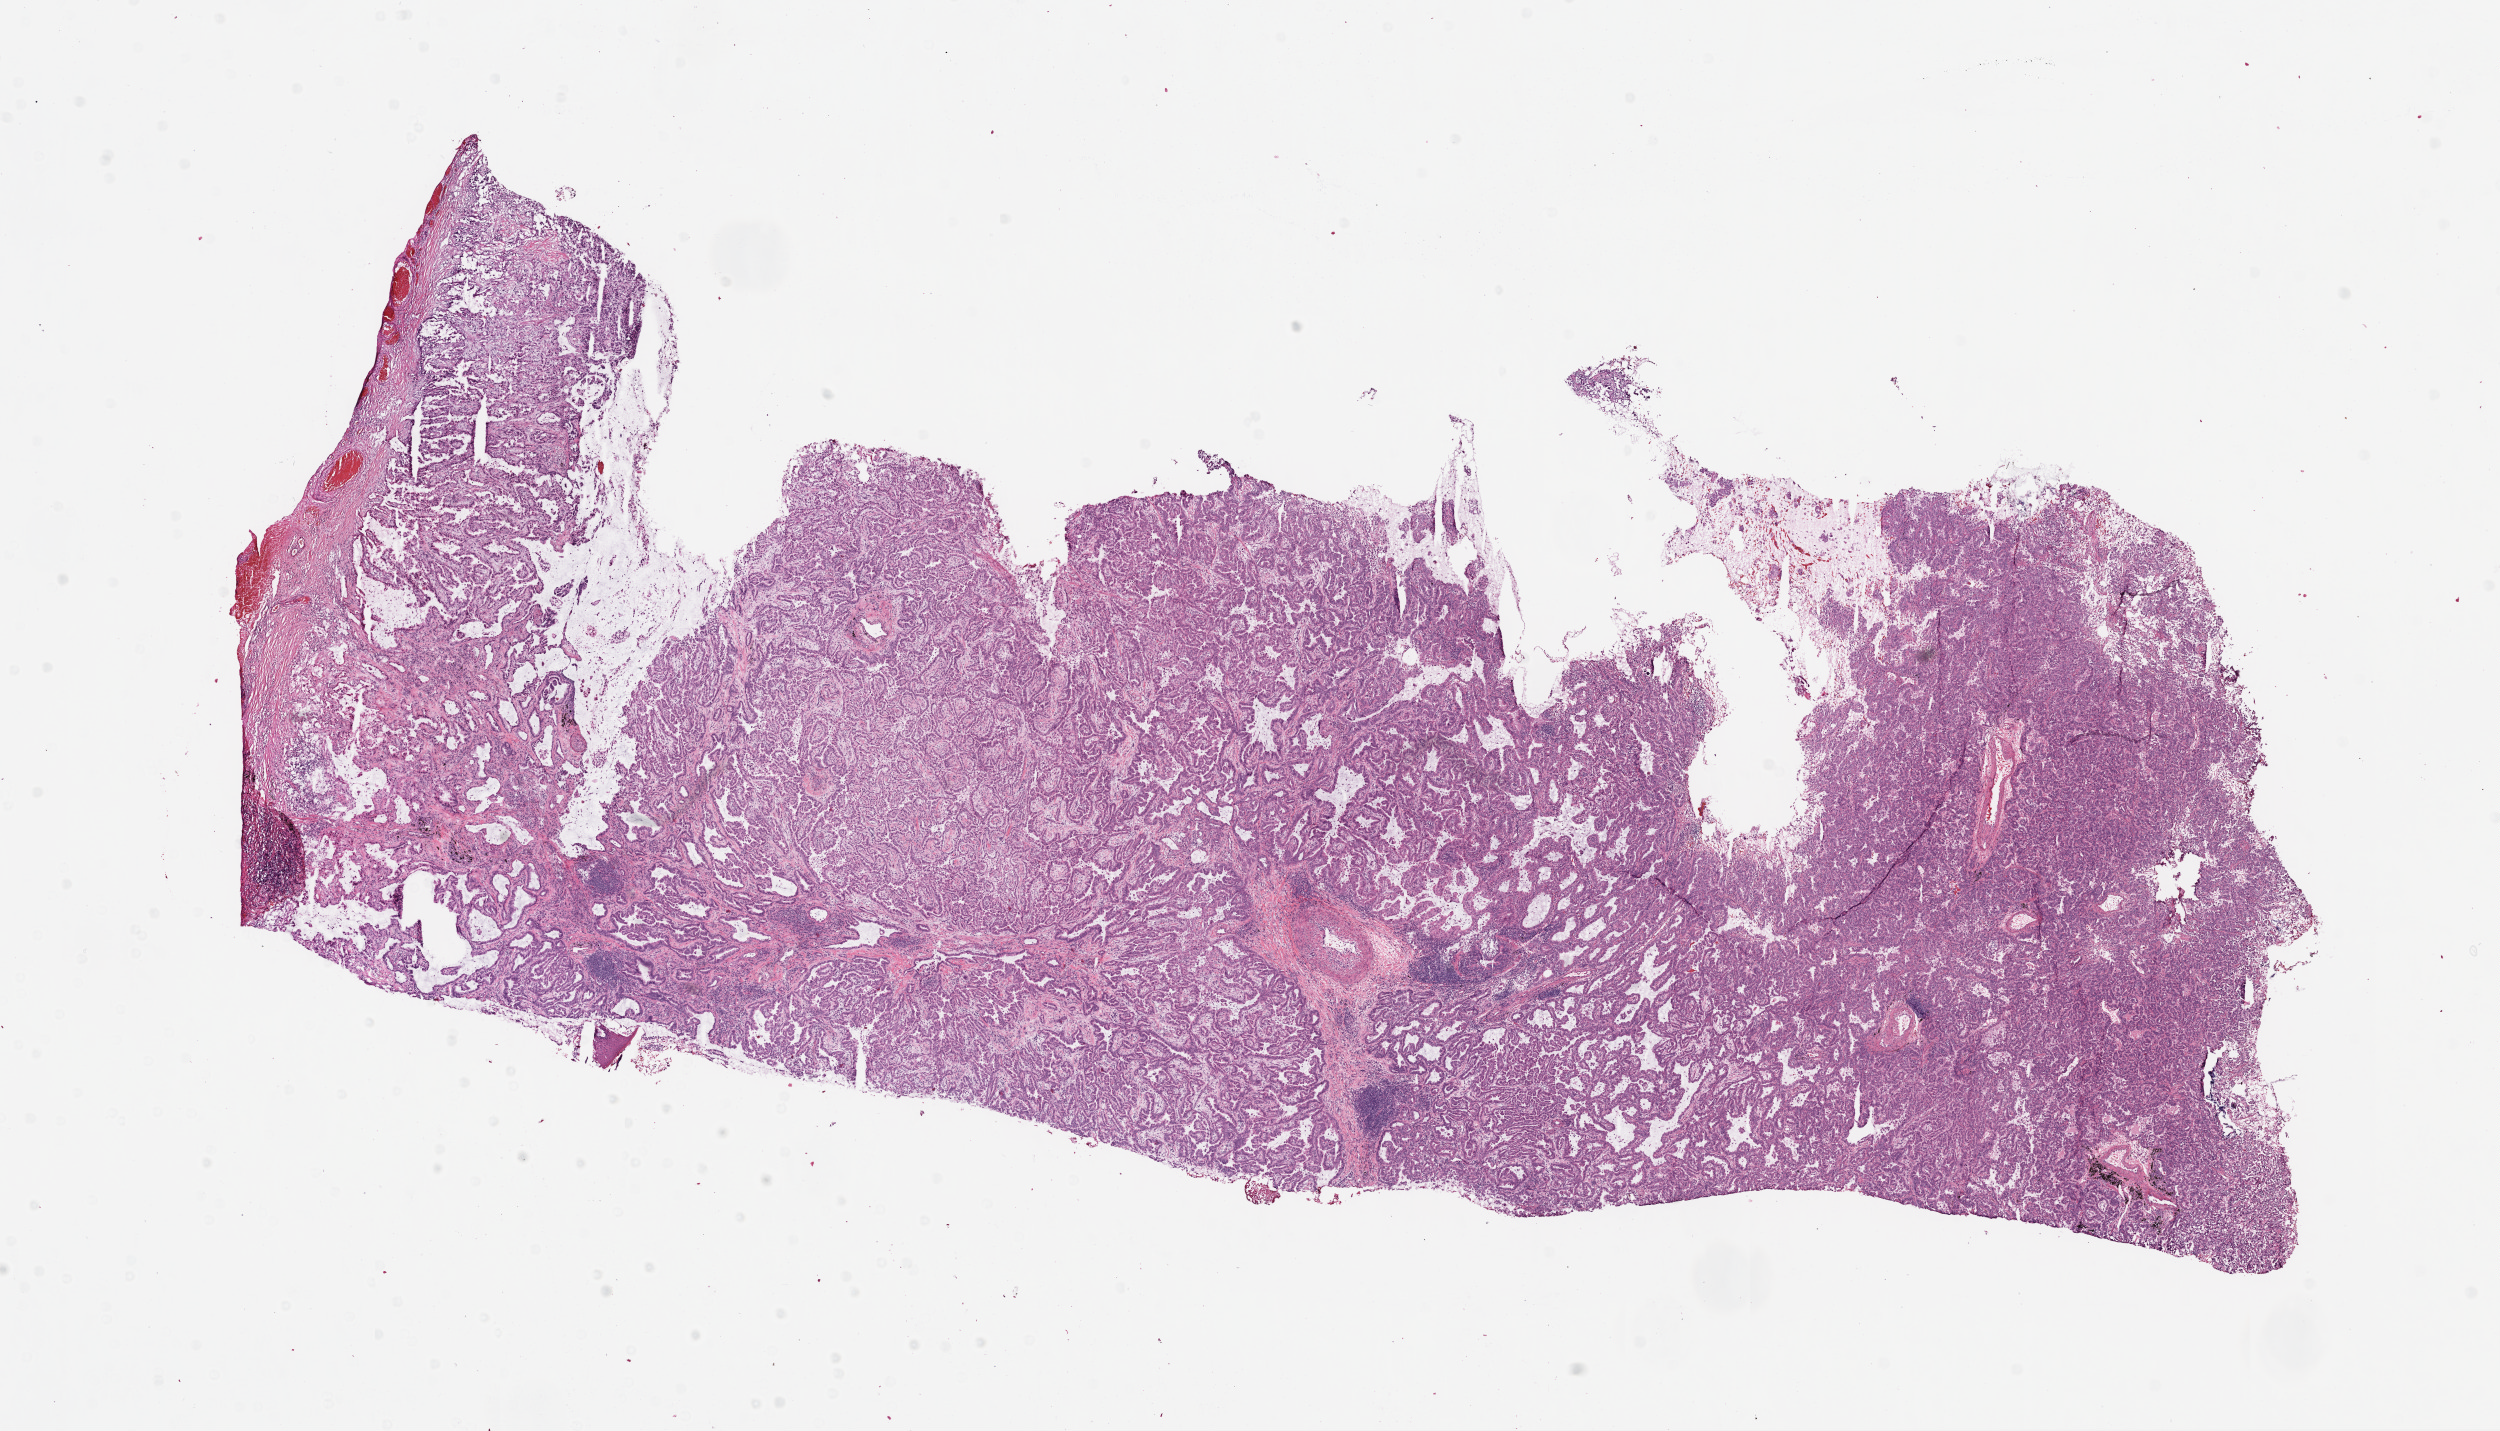
Digitized Hematoxylin and eosin (H&E) stained tissue section (whole slide) — low-resolution overview of the scanned area, about 20.1 x 11.5 mm (from a 20x scan); frozen section from the top of the tissue portion; primary tumour sample from the lung. Patient: male, age at initial diagnosis 57 years. Composition of this section per pathologist review: tumour cells 60%, tumour nuclei 80%, normal cells 0%, stromal cells 40%, necrosis 0%.
AJCC pathologic stage: IB. Diagnosis: Adenocarcinoma, NOS (upper lobe, lung).